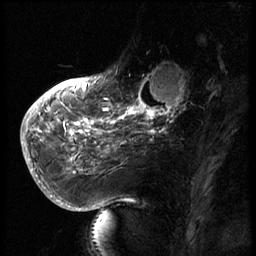
Breast MRI (dynamic contrast-enhanced), one sagittal slice. Position 20 of 66 along the scan axis. 3 images stored at this slice position (order not interpretable as contrast timing). 1.5 T. TE 4.2 ms, TR 8.9 ms. 2.5 mm slice thickness. 256 × 256 image matrix, field of view 200 × 200 mm. Female patient, age 56 years. From the clinical record (not read from this slice): setting: breast cancer imaged before/during neoadjuvant chemotherapy.
Annotated regions visible in this slice (semi-automatically segmented with operator editing):
- analysis volume of interest (the breast-tissue region the enhancement analysis was run in; not a lesion): bounding box (x1, y1, x2, y2) in pixels: (129, 62, 194, 127)
- tumour enhancement mask (voxels above the 140 % enhancement threshold inside the analysis volume of interest): (129, 68, 187, 127)